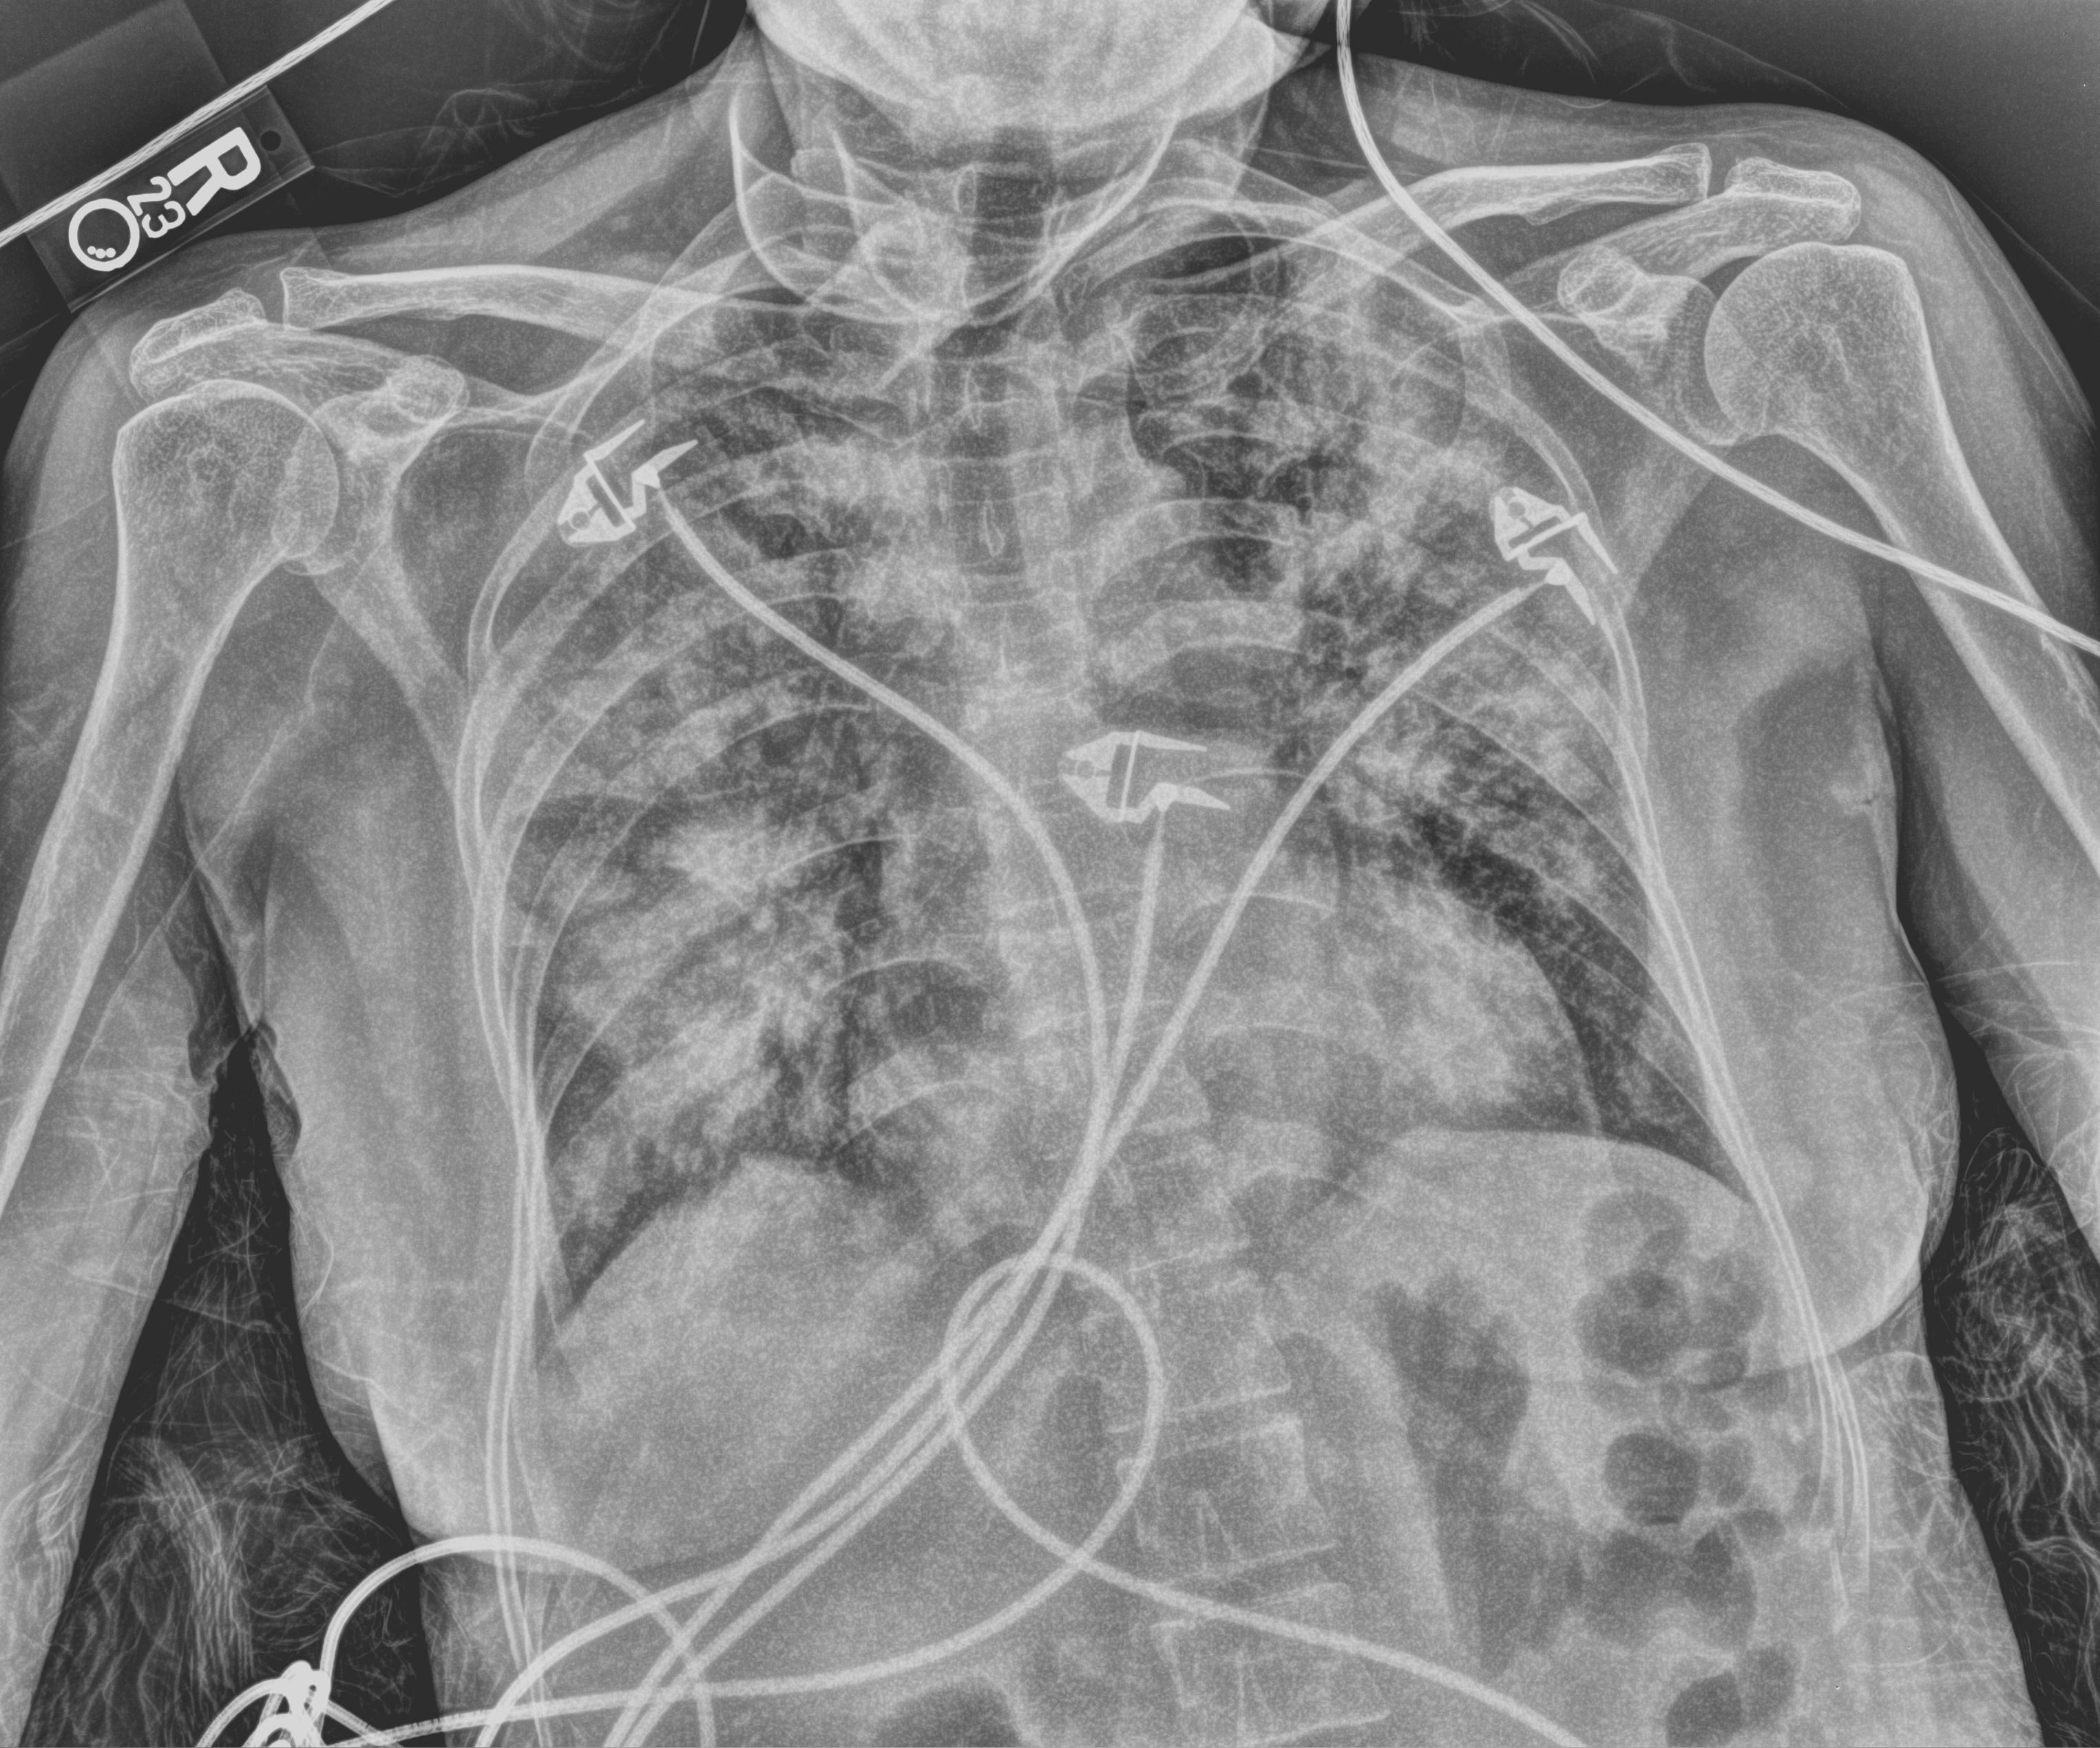
Bedside chest radiograph (computed radiography). Patient hospitalised with COVID-19; female, aged 60–74 years.
Hospital-stay facts (about this admission, not read from this image; timing relative to this image not recorded):
- admitted to intensive care during this hospital stay: yes